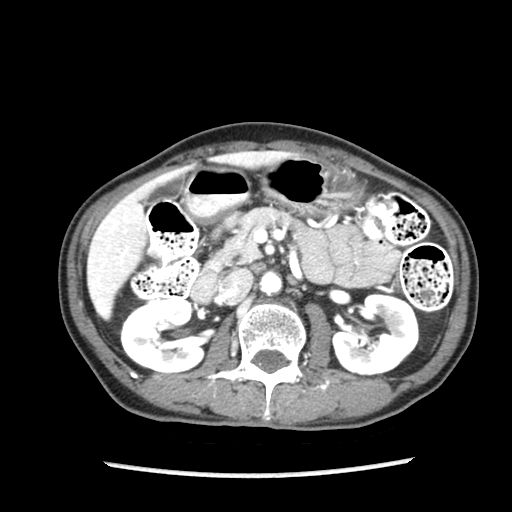
Contrast-enhanced abdominal CT (liver protocol), one axial slice; slice 41 of 87 in the series (ordered by position); soft-tissue window (W 400 / L 40 HU); 2.5 mm slice thickness; 512 × 512 image matrix, field of view 300 × 300 mm. Case-level facts recorded for this patient, not image findings: diagnosis: hepatocellular carcinoma (patient treated with transarterial chemoembolisation; whether this scan precedes or follows treatment is not stated here); TNM stage (as recorded): Stage-IIIB; Child-Pugh class: A.
Structures marked on this image (semi-automatic segmentation, software-assisted and operator-edited):
- liver parenchyma outside the tumour (the mass and vessels are separate outlines, so this box may not span the whole liver): bounding box (x1, y1, x2, y2) in pixels: (88, 178, 167, 318)
- liver vessels: (89, 215, 128, 314)